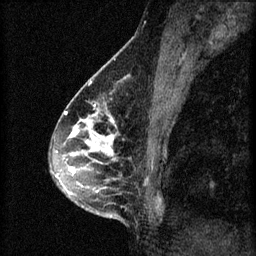
Breast MRI (dynamic contrast-enhanced), one sagittal slice. Position 29 of 60 along the scan axis. 3 images stored at this slice position (order not interpretable as contrast timing). 1.5 T. TE 4.2 ms, TR 8.2 ms. 2 mm slice thickness. 256 × 256 image matrix, field of view 180 × 180 mm. Patient: female, 45 years.
Annotated regions visible in this slice (semi-automatically segmented with operator editing):
- analysis volume of interest (the breast-tissue region the enhancement analysis was run in; not a lesion): bounding box <54,104,159,217> (left, top, right, bottom; pixels)
- tumour enhancement mask (voxels above the 70 % enhancement threshold inside the analysis volume of interest): <56,104,117,197>